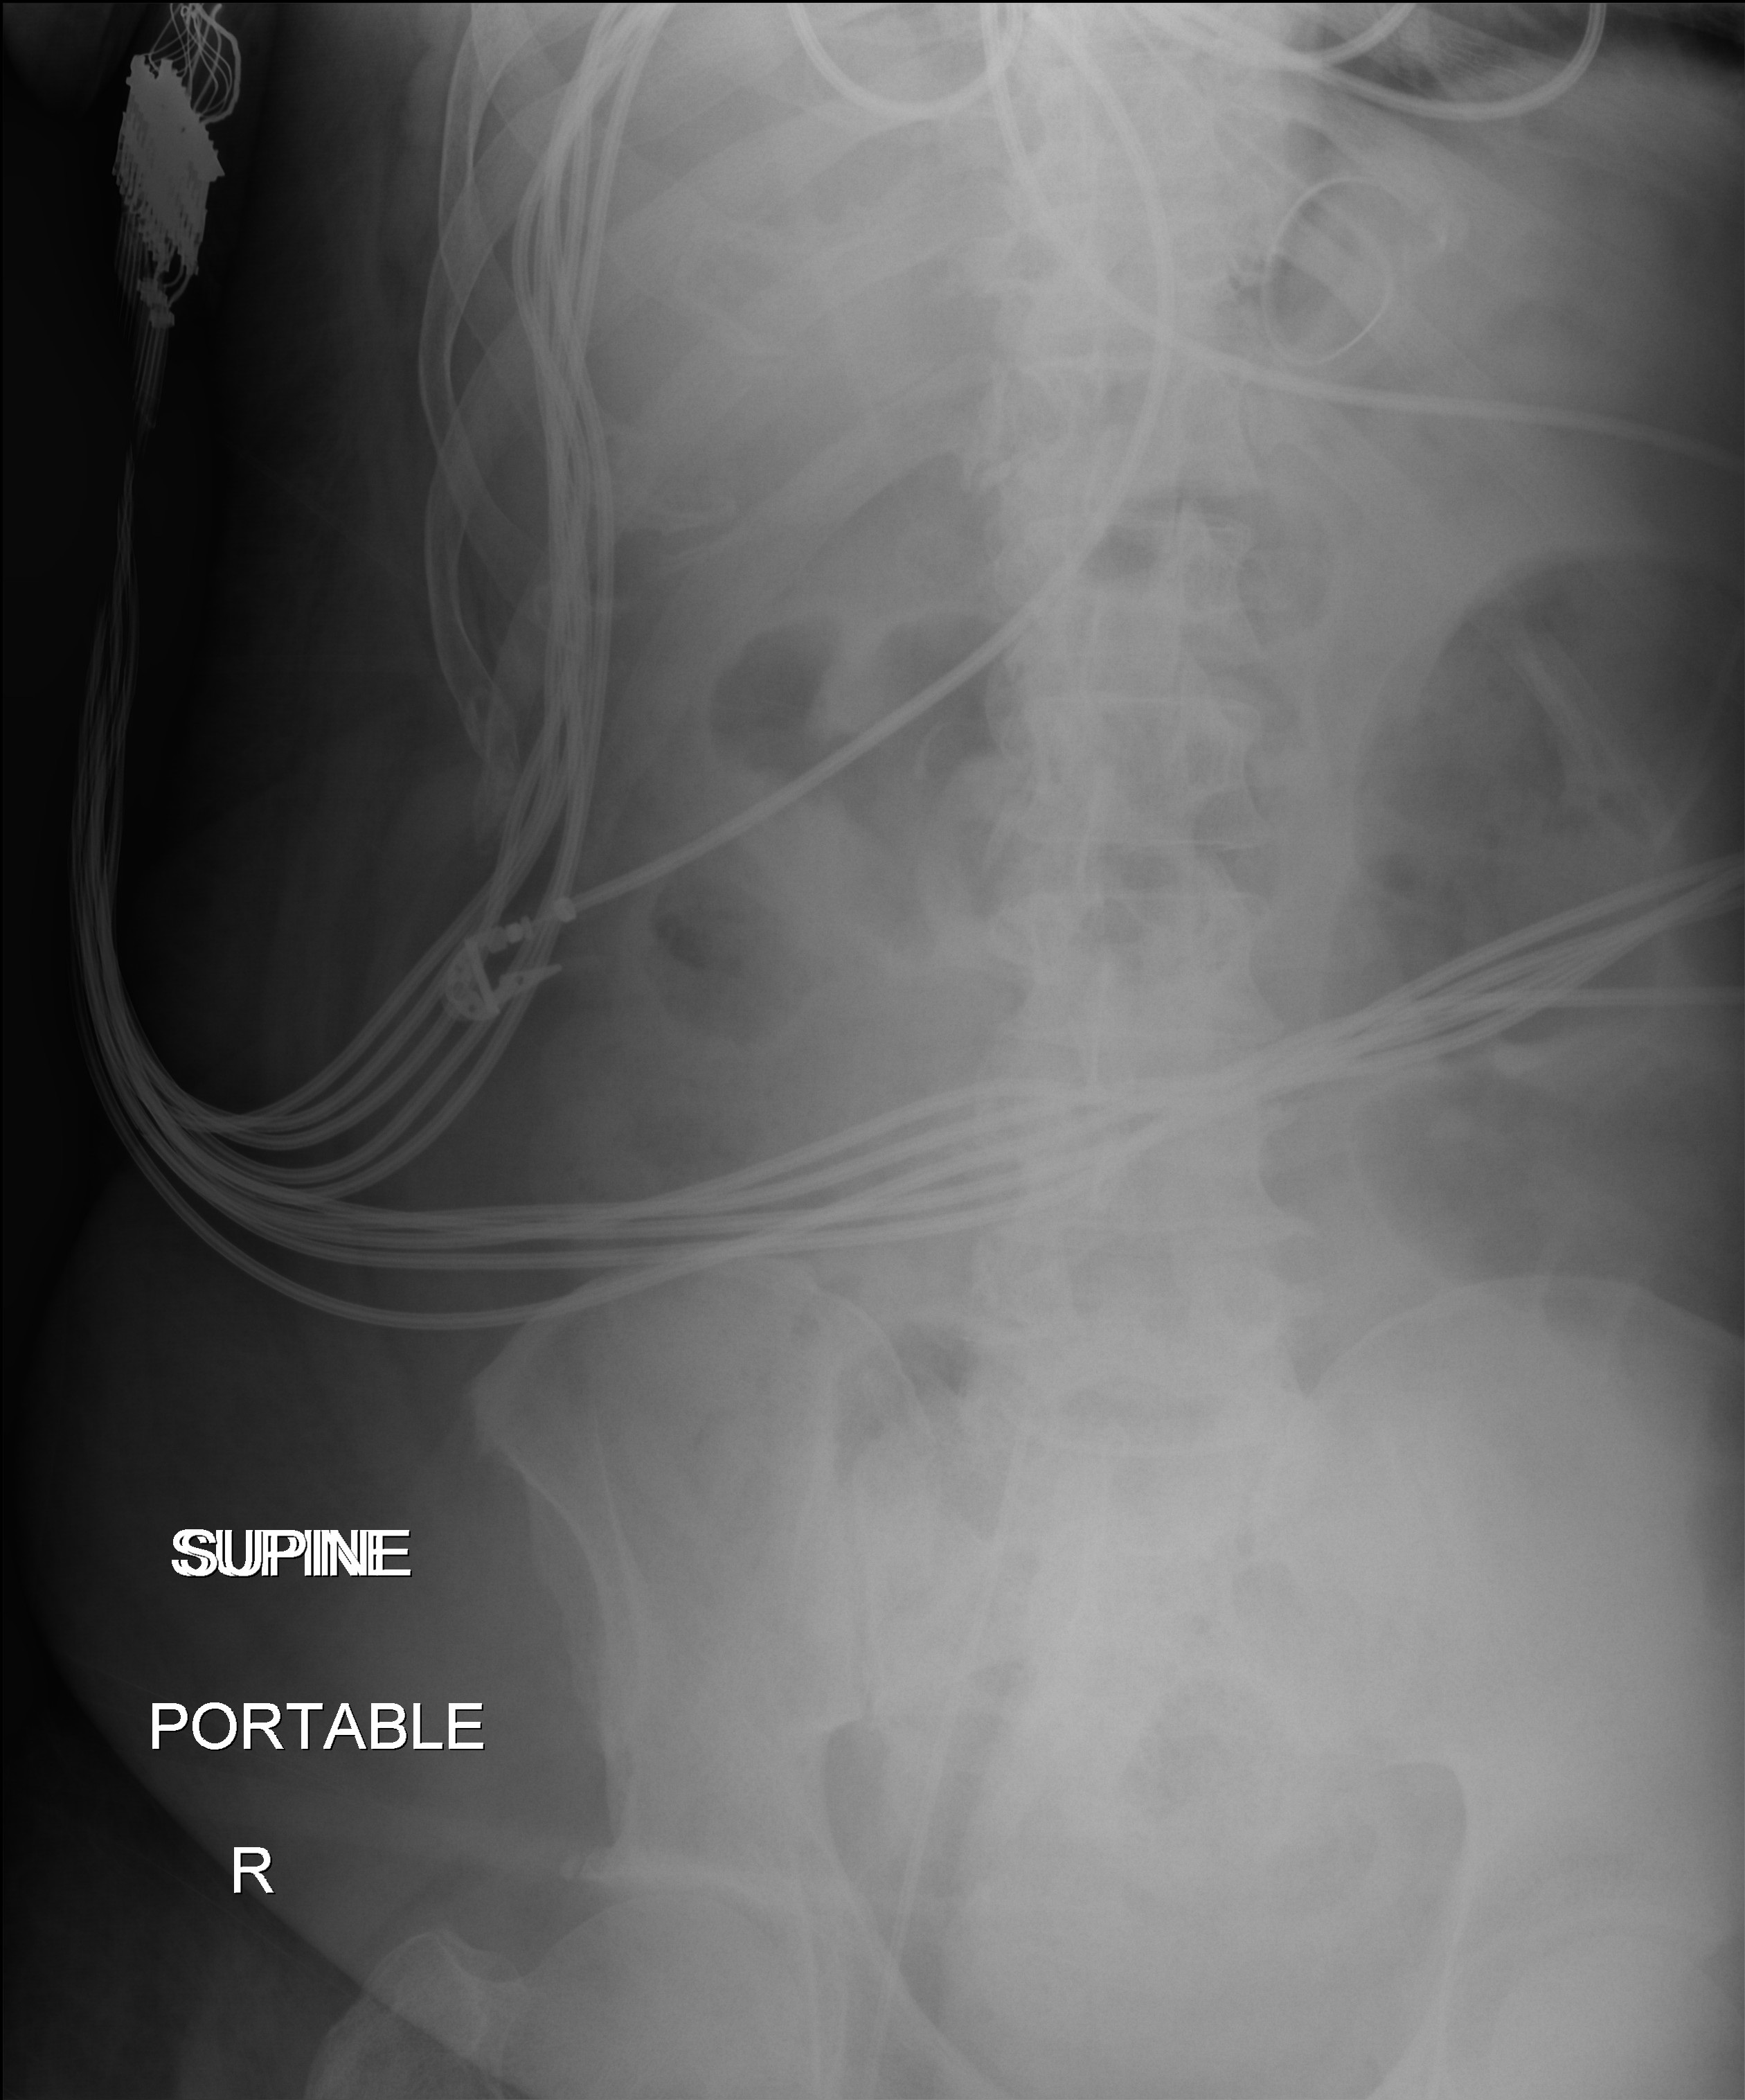
Portable abdomen radiograph, anteroposterior (AP) projection. Patient hospitalised with COVID-19, aged 18–59 years.
From the hospital-stay record, not from the radiograph (when in the stay this image was taken is not recorded): mechanically ventilated during this hospital stay: yes; length of hospital stay: 37 days.